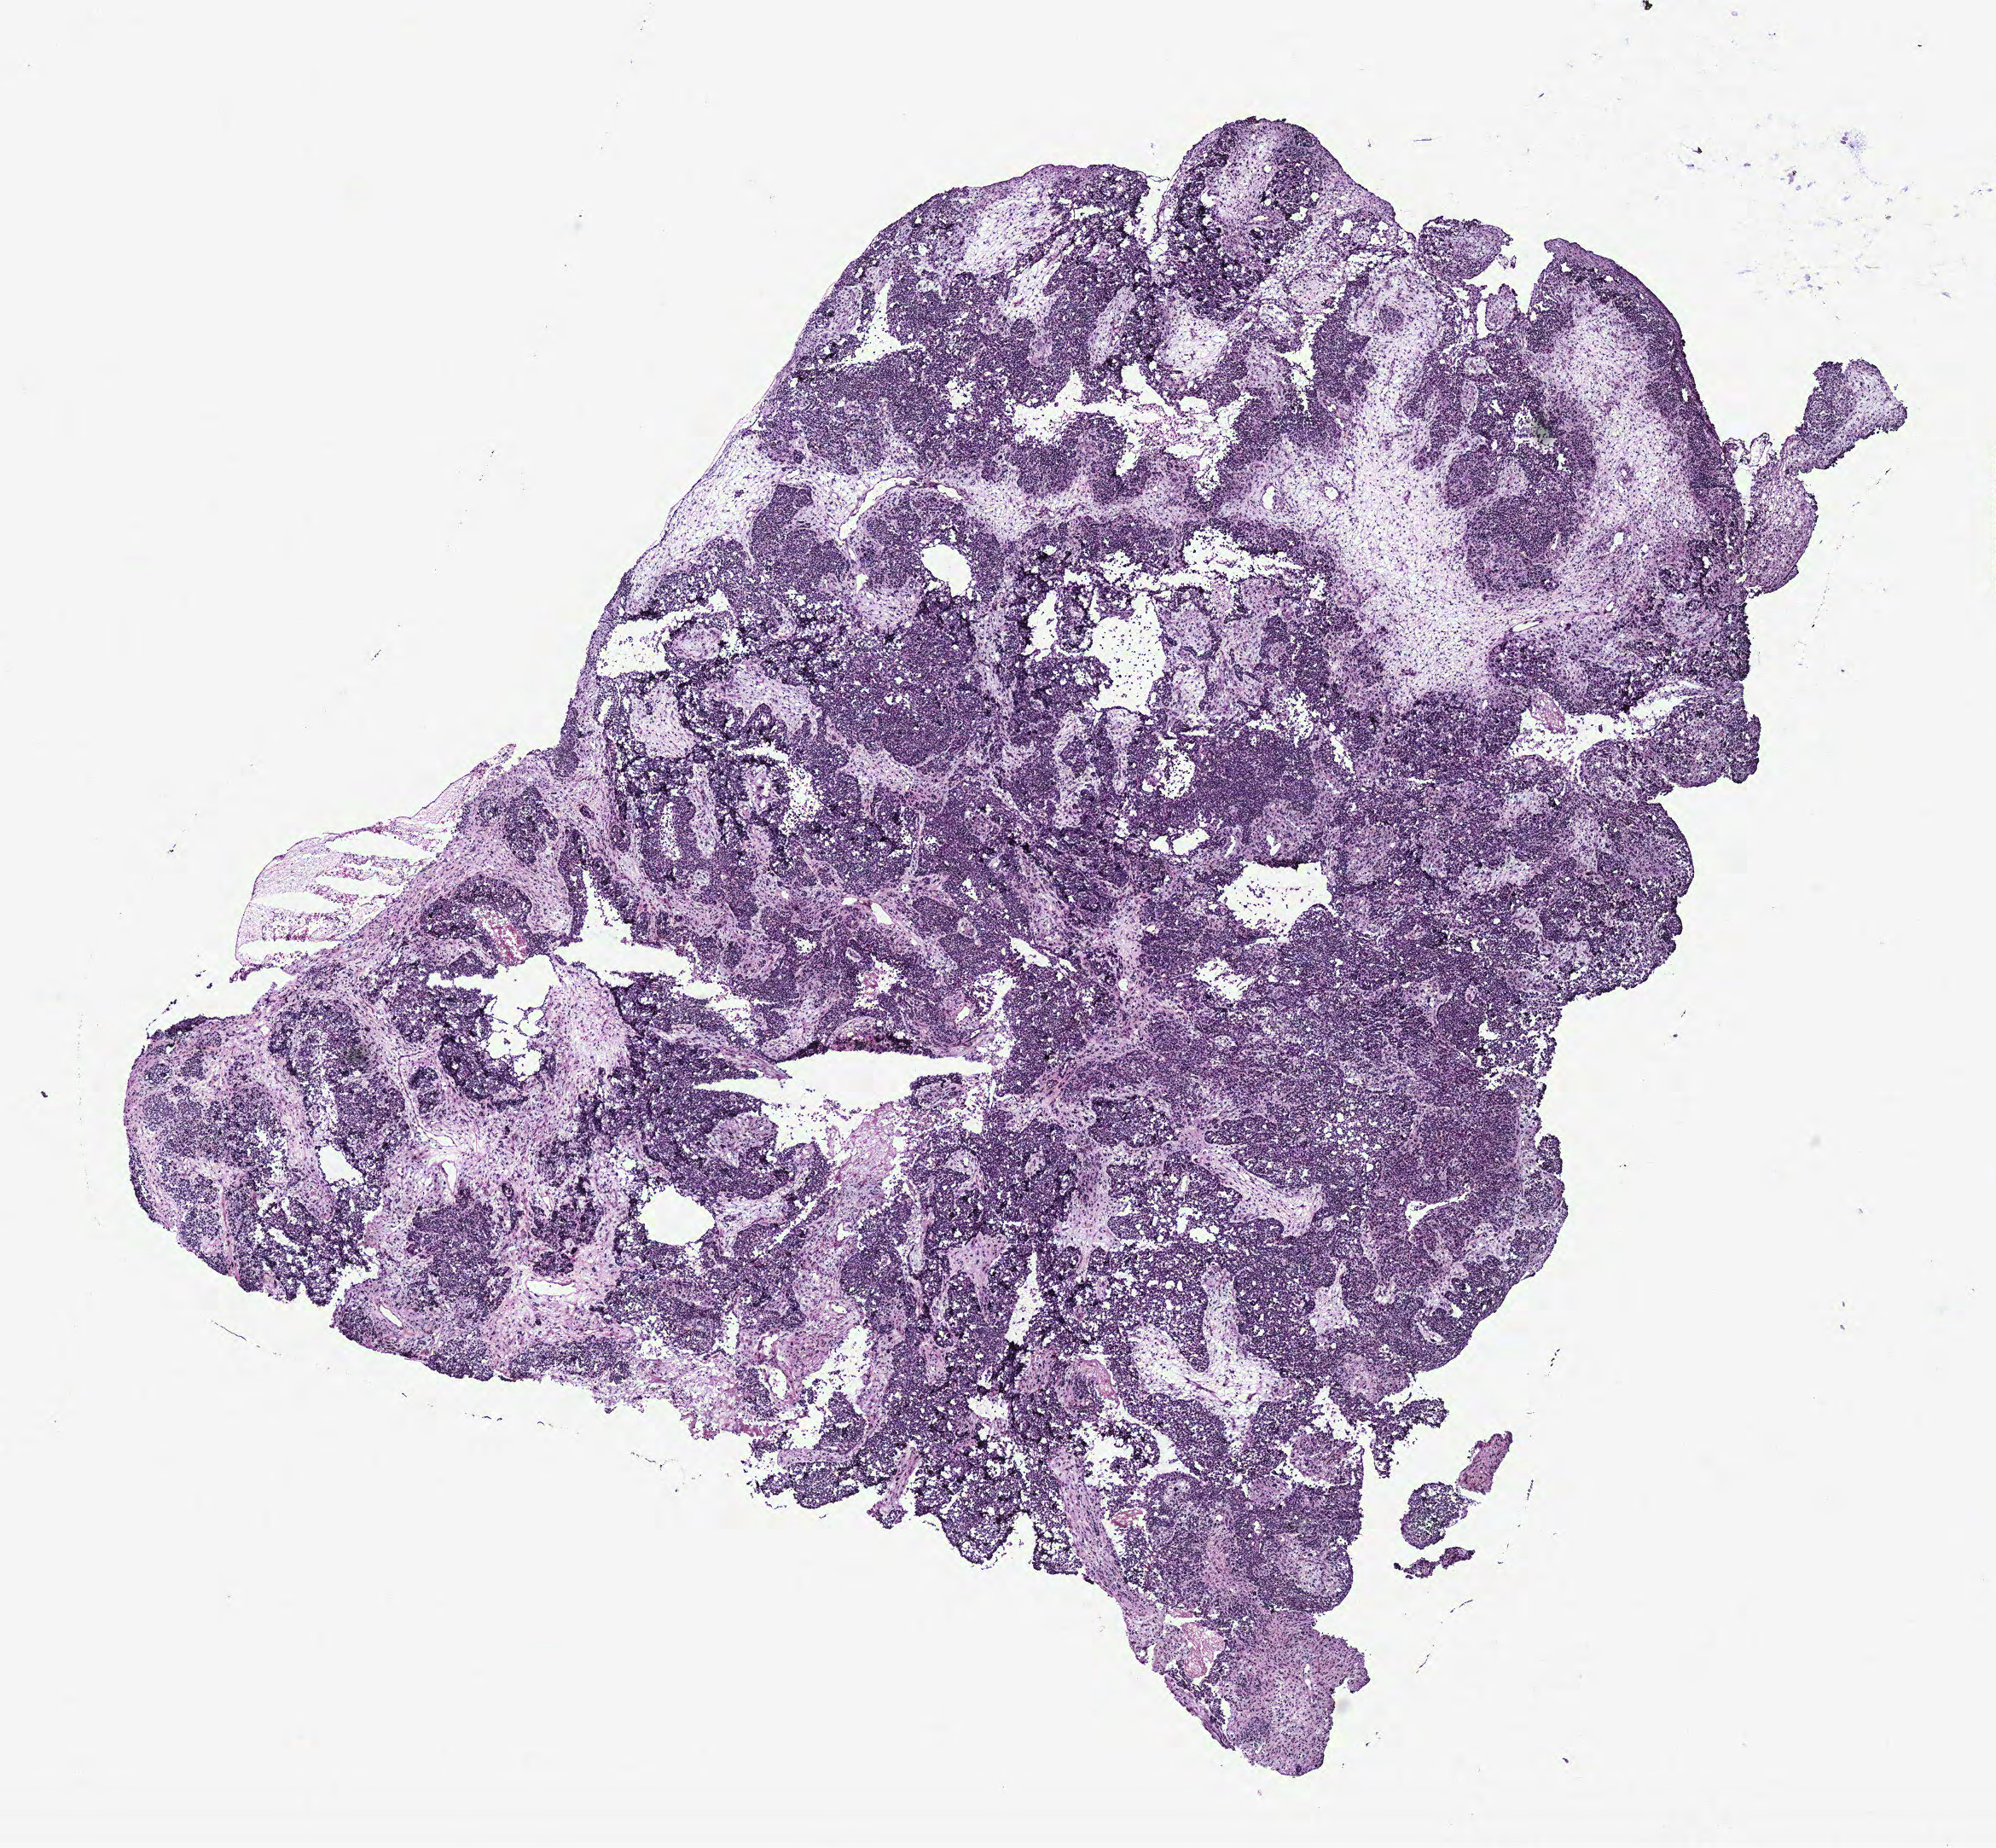
Whole-slide histology image, Hematoxylin and eosin (H&E) stained — low-resolution overview of the scanned area, about 9.4 x 8.7 mm (slide scanned at 40x); ovary, tissue type not recorded. Female patient.
• patient diagnosis: Serous adenocarcinoma, NOS